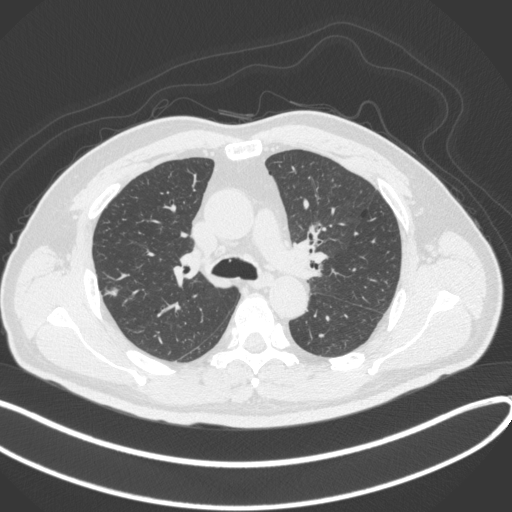
Chest CT, one axial slice; position 226 of 373 along the scan axis; 120 kVp; lung window (W 1500 / L -600 HU); 1 mm slice thickness; 512 × 512 image matrix, field of view 400 × 400 mm. Patient: male, 60 years. From the clinical record (not read from this slice): clinical TNM (as recorded): T1c N0 M0.
Outlined on this slice (rectangle marked by the reading radiologist):
- lung tumour (recorded histology: adenocarcinoma): box from (x=101, y=285) to (x=119, y=300) px